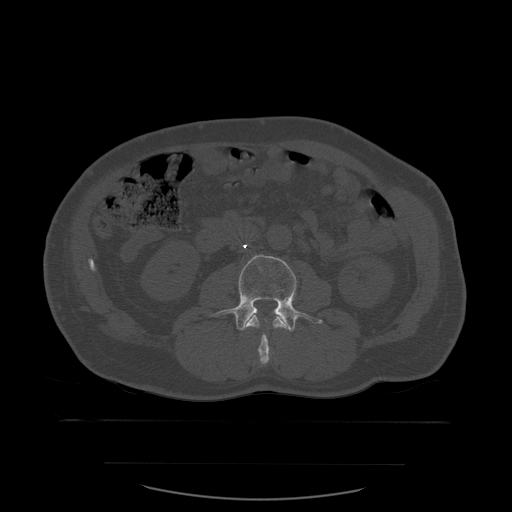
CT including the spine, one axial slice. Slice 200 of 590 in the series (ordered by position). Bone window (W 1800 / L 400 HU). 512 × 512 image matrix, field of view 479 × 479 mm. Patient age 71 years. From the clinical record (not read from this slice): primary cancer: lung.
Outlined on this slice (semi-automatically segmented with operator editing):
- L2 vertebra: bounding box [x1, y1, x2, y2] px = [245, 309, 291, 365]
- L3 vertebra: [214, 254, 323, 332]